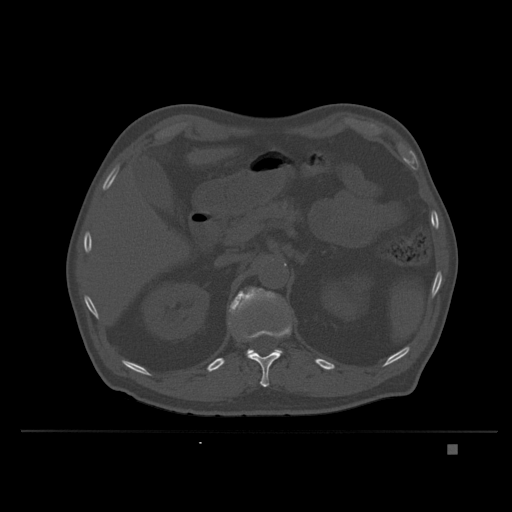
CT including the spine, one axial slice; slice 152 of 435 in the series (ordered by position); bone window (W 1800 / L 400 HU); 1.5 mm slice thickness; 512 × 512 image matrix, field of view 434 × 434 mm. Male patient, age 73 years. Case-level facts recorded for this patient, not image findings: primary cancer: skin.
Outlined on this slice (semi-automatically segmented with operator editing):
- L1 vertebra: bounding box [x1, y1, x2, y2] px = [228, 286, 283, 359]
- T12 vertebra: [228, 322, 292, 387]